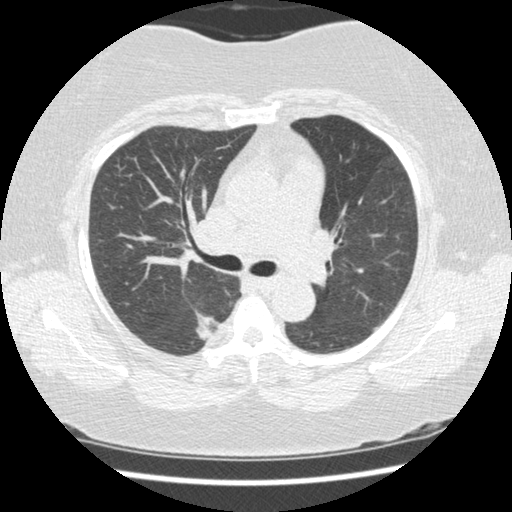
Chest CT (low-dose screening protocol), one axial image; second annual screen; lung window (W 1500 / L -600 HU); standard (soft-tissue) reconstruction kernel (STANDARD); slice 67 of 210 in the series. Female participant, aged 58 years at enrolment. Current smoker at enrolment.
Expert-annotated lung lesion, bounding box [x1, y1, x2, y2] px = [189, 308, 229, 357]. Screening reader's record for this exam (one nodule recorded; not confirmed to be the boxed lesion): non-calcified nodule or mass ≥4 mm, right lower lobe, 15 × 15 mm, spiculated (stellate) margins, soft tissue attenuation, pre-existing on the prior screen: yes; interval growth: yes. Official screen result: positive, change unspecified: nodule(s) >= 4 mm or enlarging nodule(s), mass(es), or other non-specific abnormalities suspicious for lung cancer.